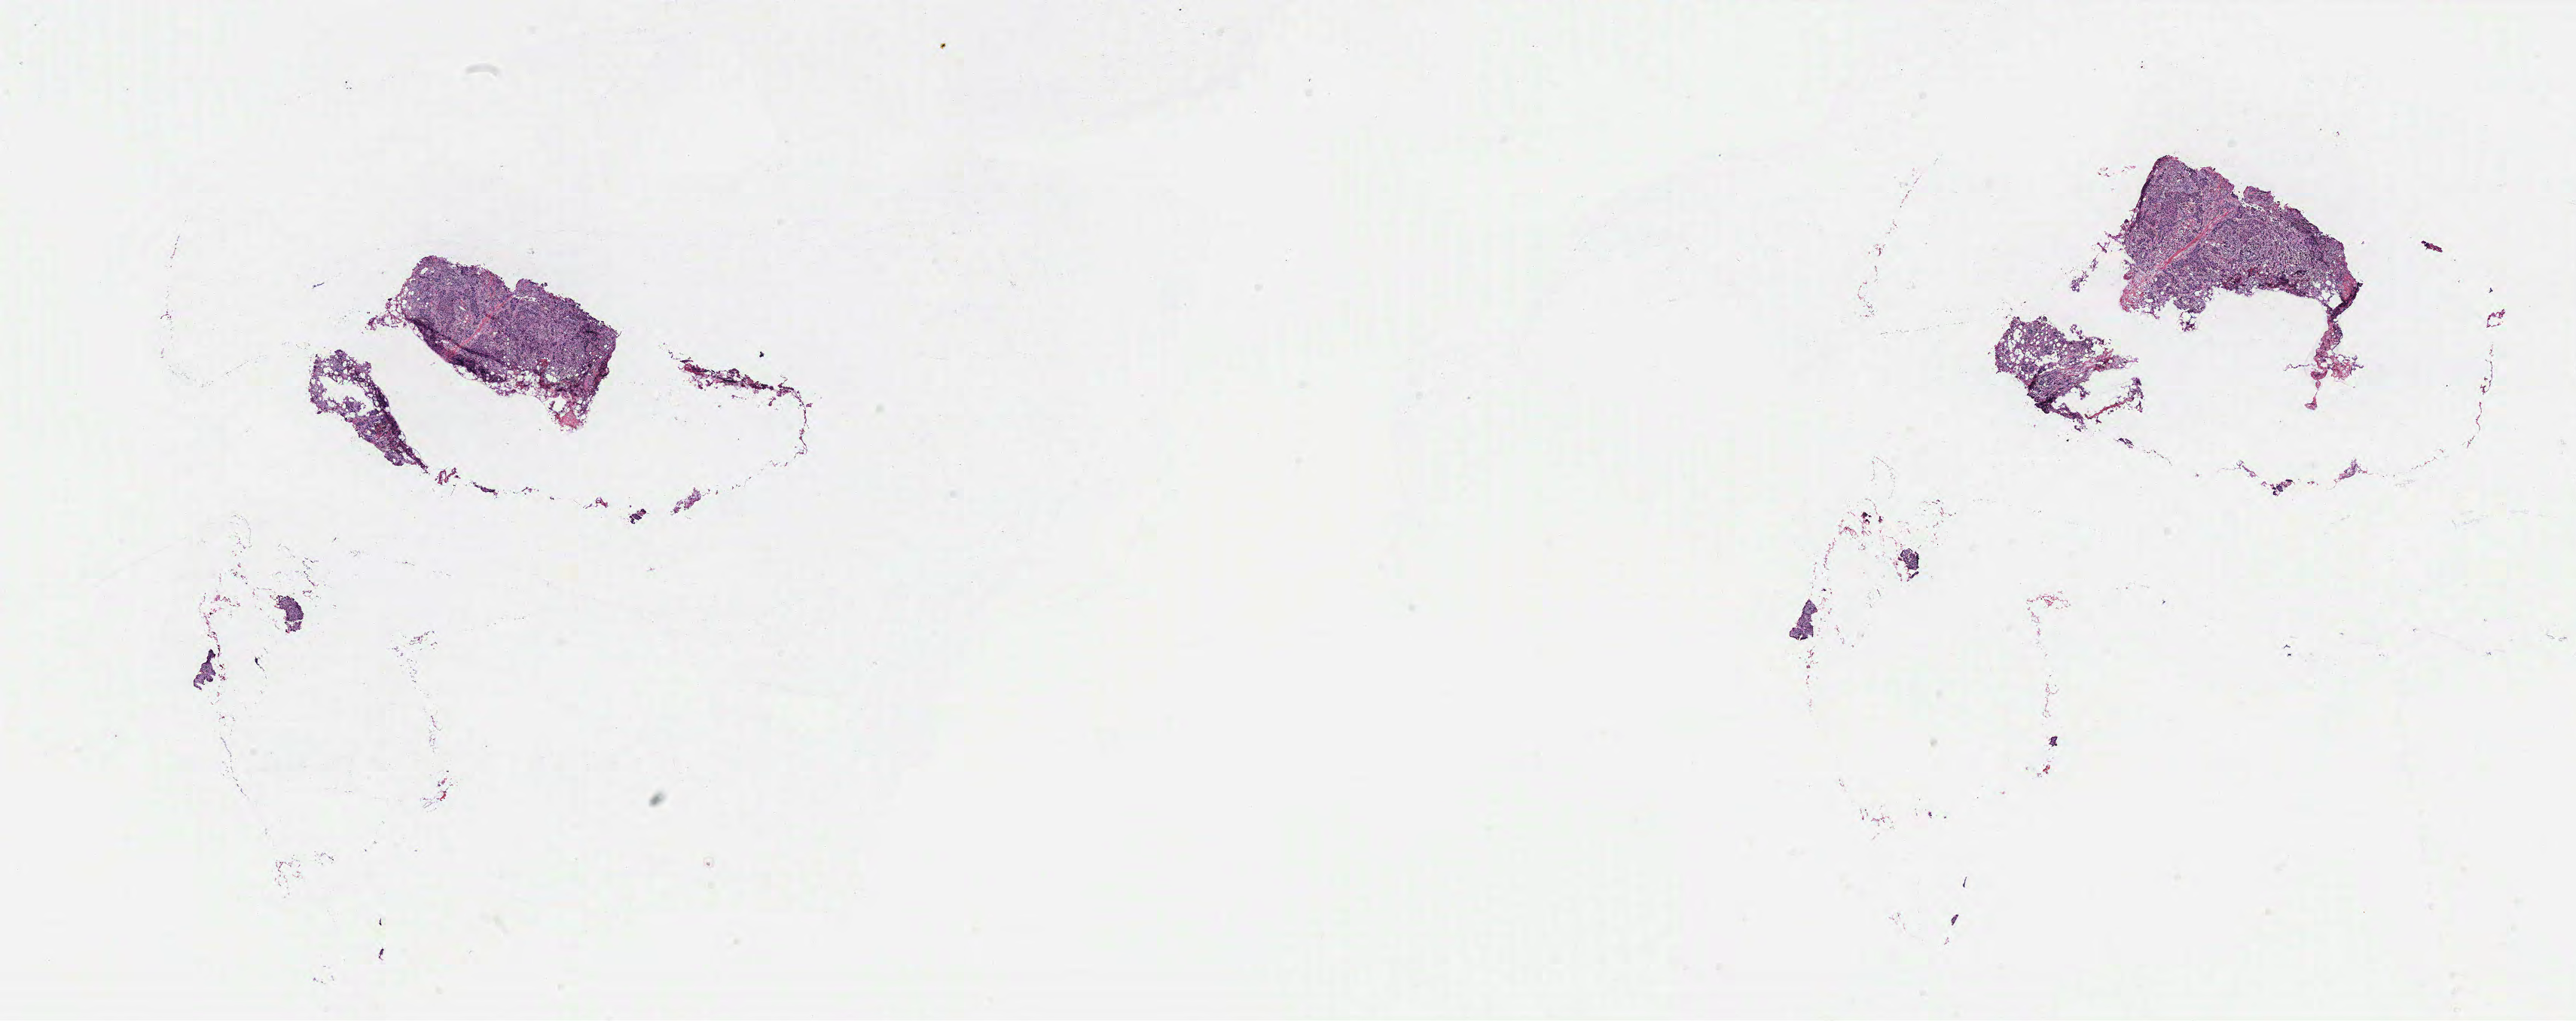
Hematoxylin and eosin (H&E) stained whole-slide image — low-resolution overview of the scanned area, about 27.4 x 10.8 mm (from a 40x scan), breast, tissue type not recorded.
Patient diagnosis (cohort enrolment): breast cancer (breast).